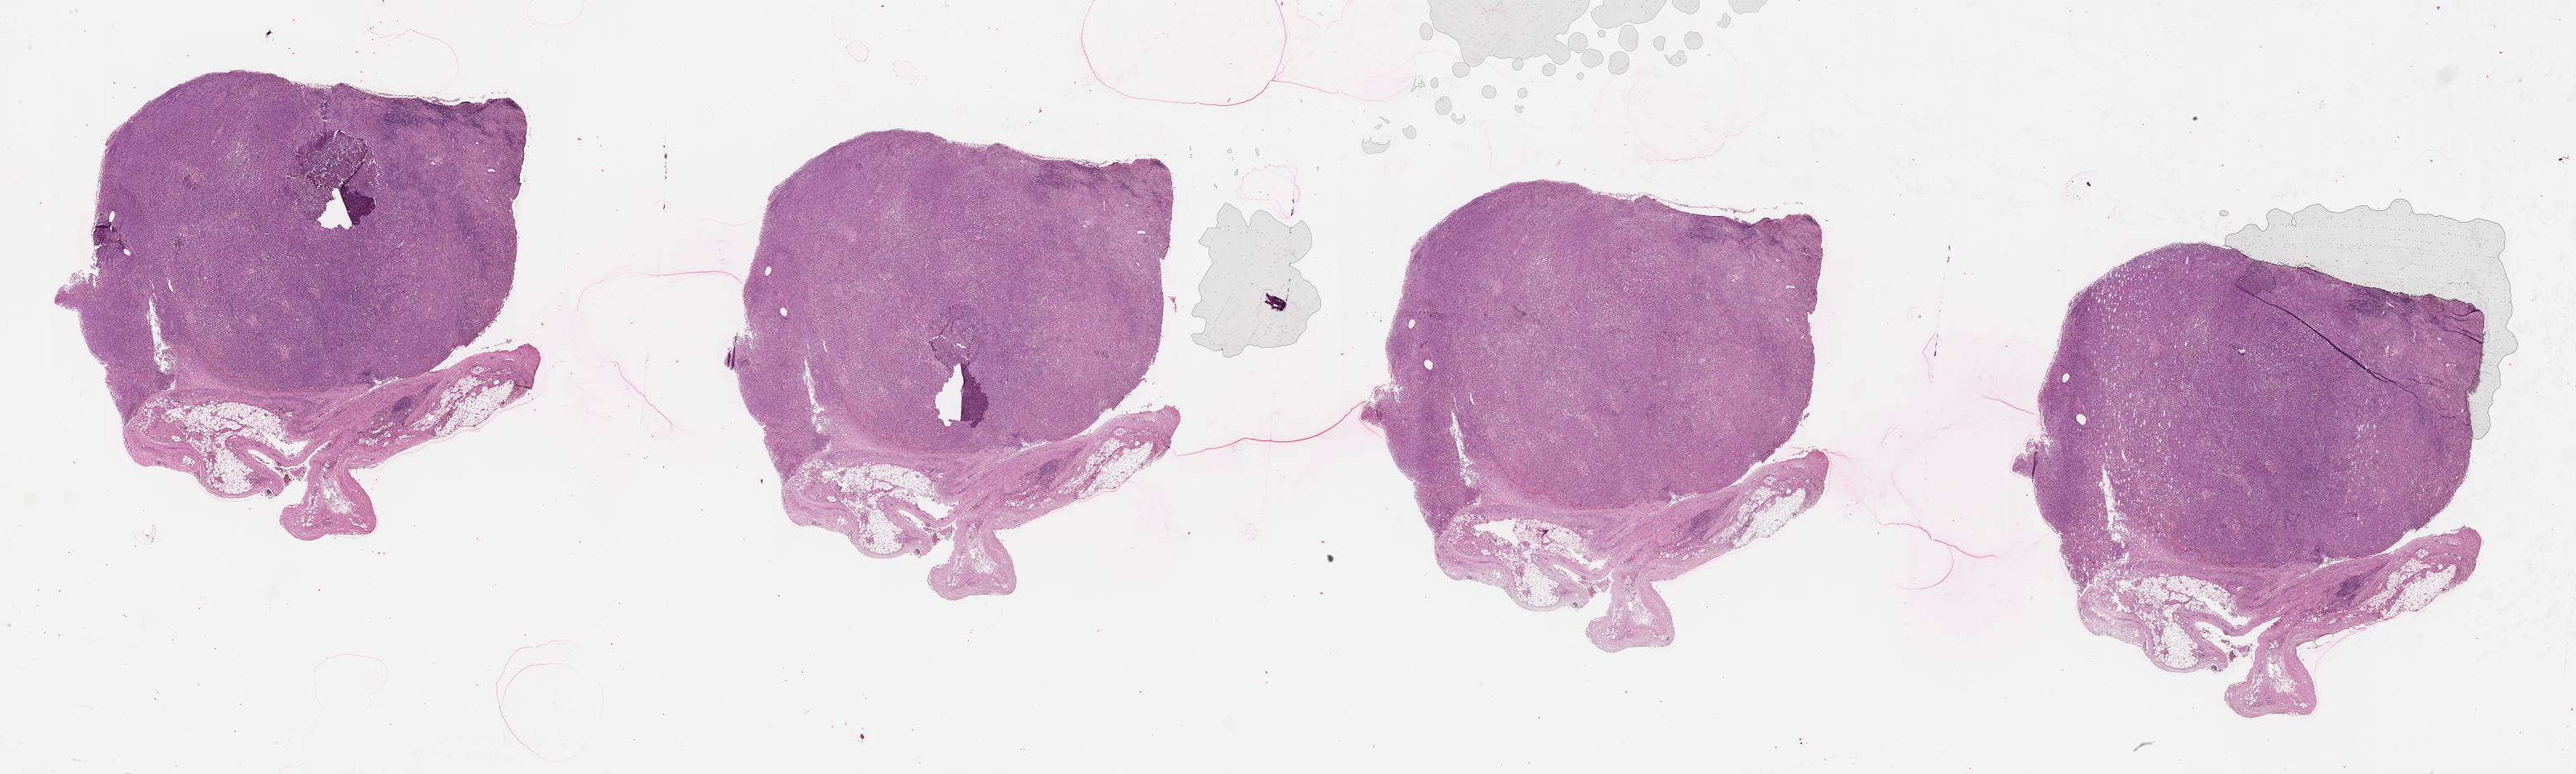
Whole-slide histology image, H&E, shown as a low-resolution overview of the whole scanned area (about 50.1 x 15.1 mm). Patient: male, age 87 years.
Patient diagnosis: Malignant melanoma, NOS.